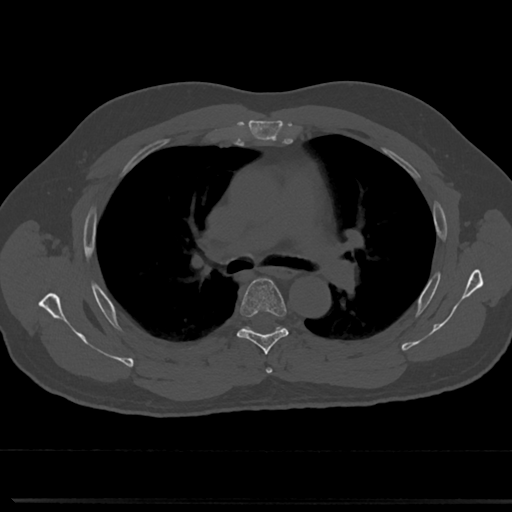
CT including the spine, one axial slice. Slice 495 of 817 in the series (ordered by position). 120 kVp. Bone window (W 1800 / L 400 HU). 0.5 mm slice thickness. 512 × 512 image matrix, field of view 355 × 355 mm. Patient: male, 61 years. From the clinical record (not read from this slice): primary cancer: prostate.
Outlined on this slice (semi-automatic segmentation, software-assisted and operator-edited):
- T4 vertebra: bounding box [x1, y1, x2, y2] px = [264, 358, 273, 374]
- T5 vertebra: [218, 277, 305, 349]